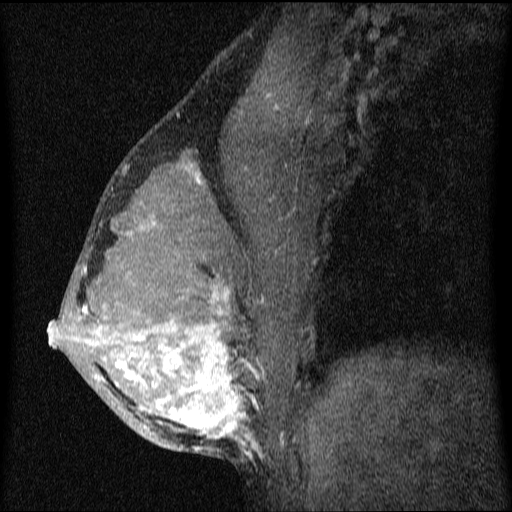
Breast MRI (dynamic contrast-enhanced), one sagittal slice; position 39 of 64 along the scan axis; dynamic contrast-enhanced series, image 2 of 4 at this slice position (ordered by acquisition); 1.5 T; TE 4.2 ms, TR 9.1 ms; 2 mm slice thickness; 512 × 512 image matrix. Patient: female, 33 years.
Structures marked on this image (semi-automatic segmentation, software-assisted and operator-edited):
- analysis volume of interest (the breast-tissue region the enhancement analysis was run in; not a lesion): box from (x=49, y=151) to (x=336, y=458) px
- tumour enhancement mask (voxels above the 70 % enhancement threshold inside the analysis volume of interest): (x=49, y=173)–(x=263, y=458)